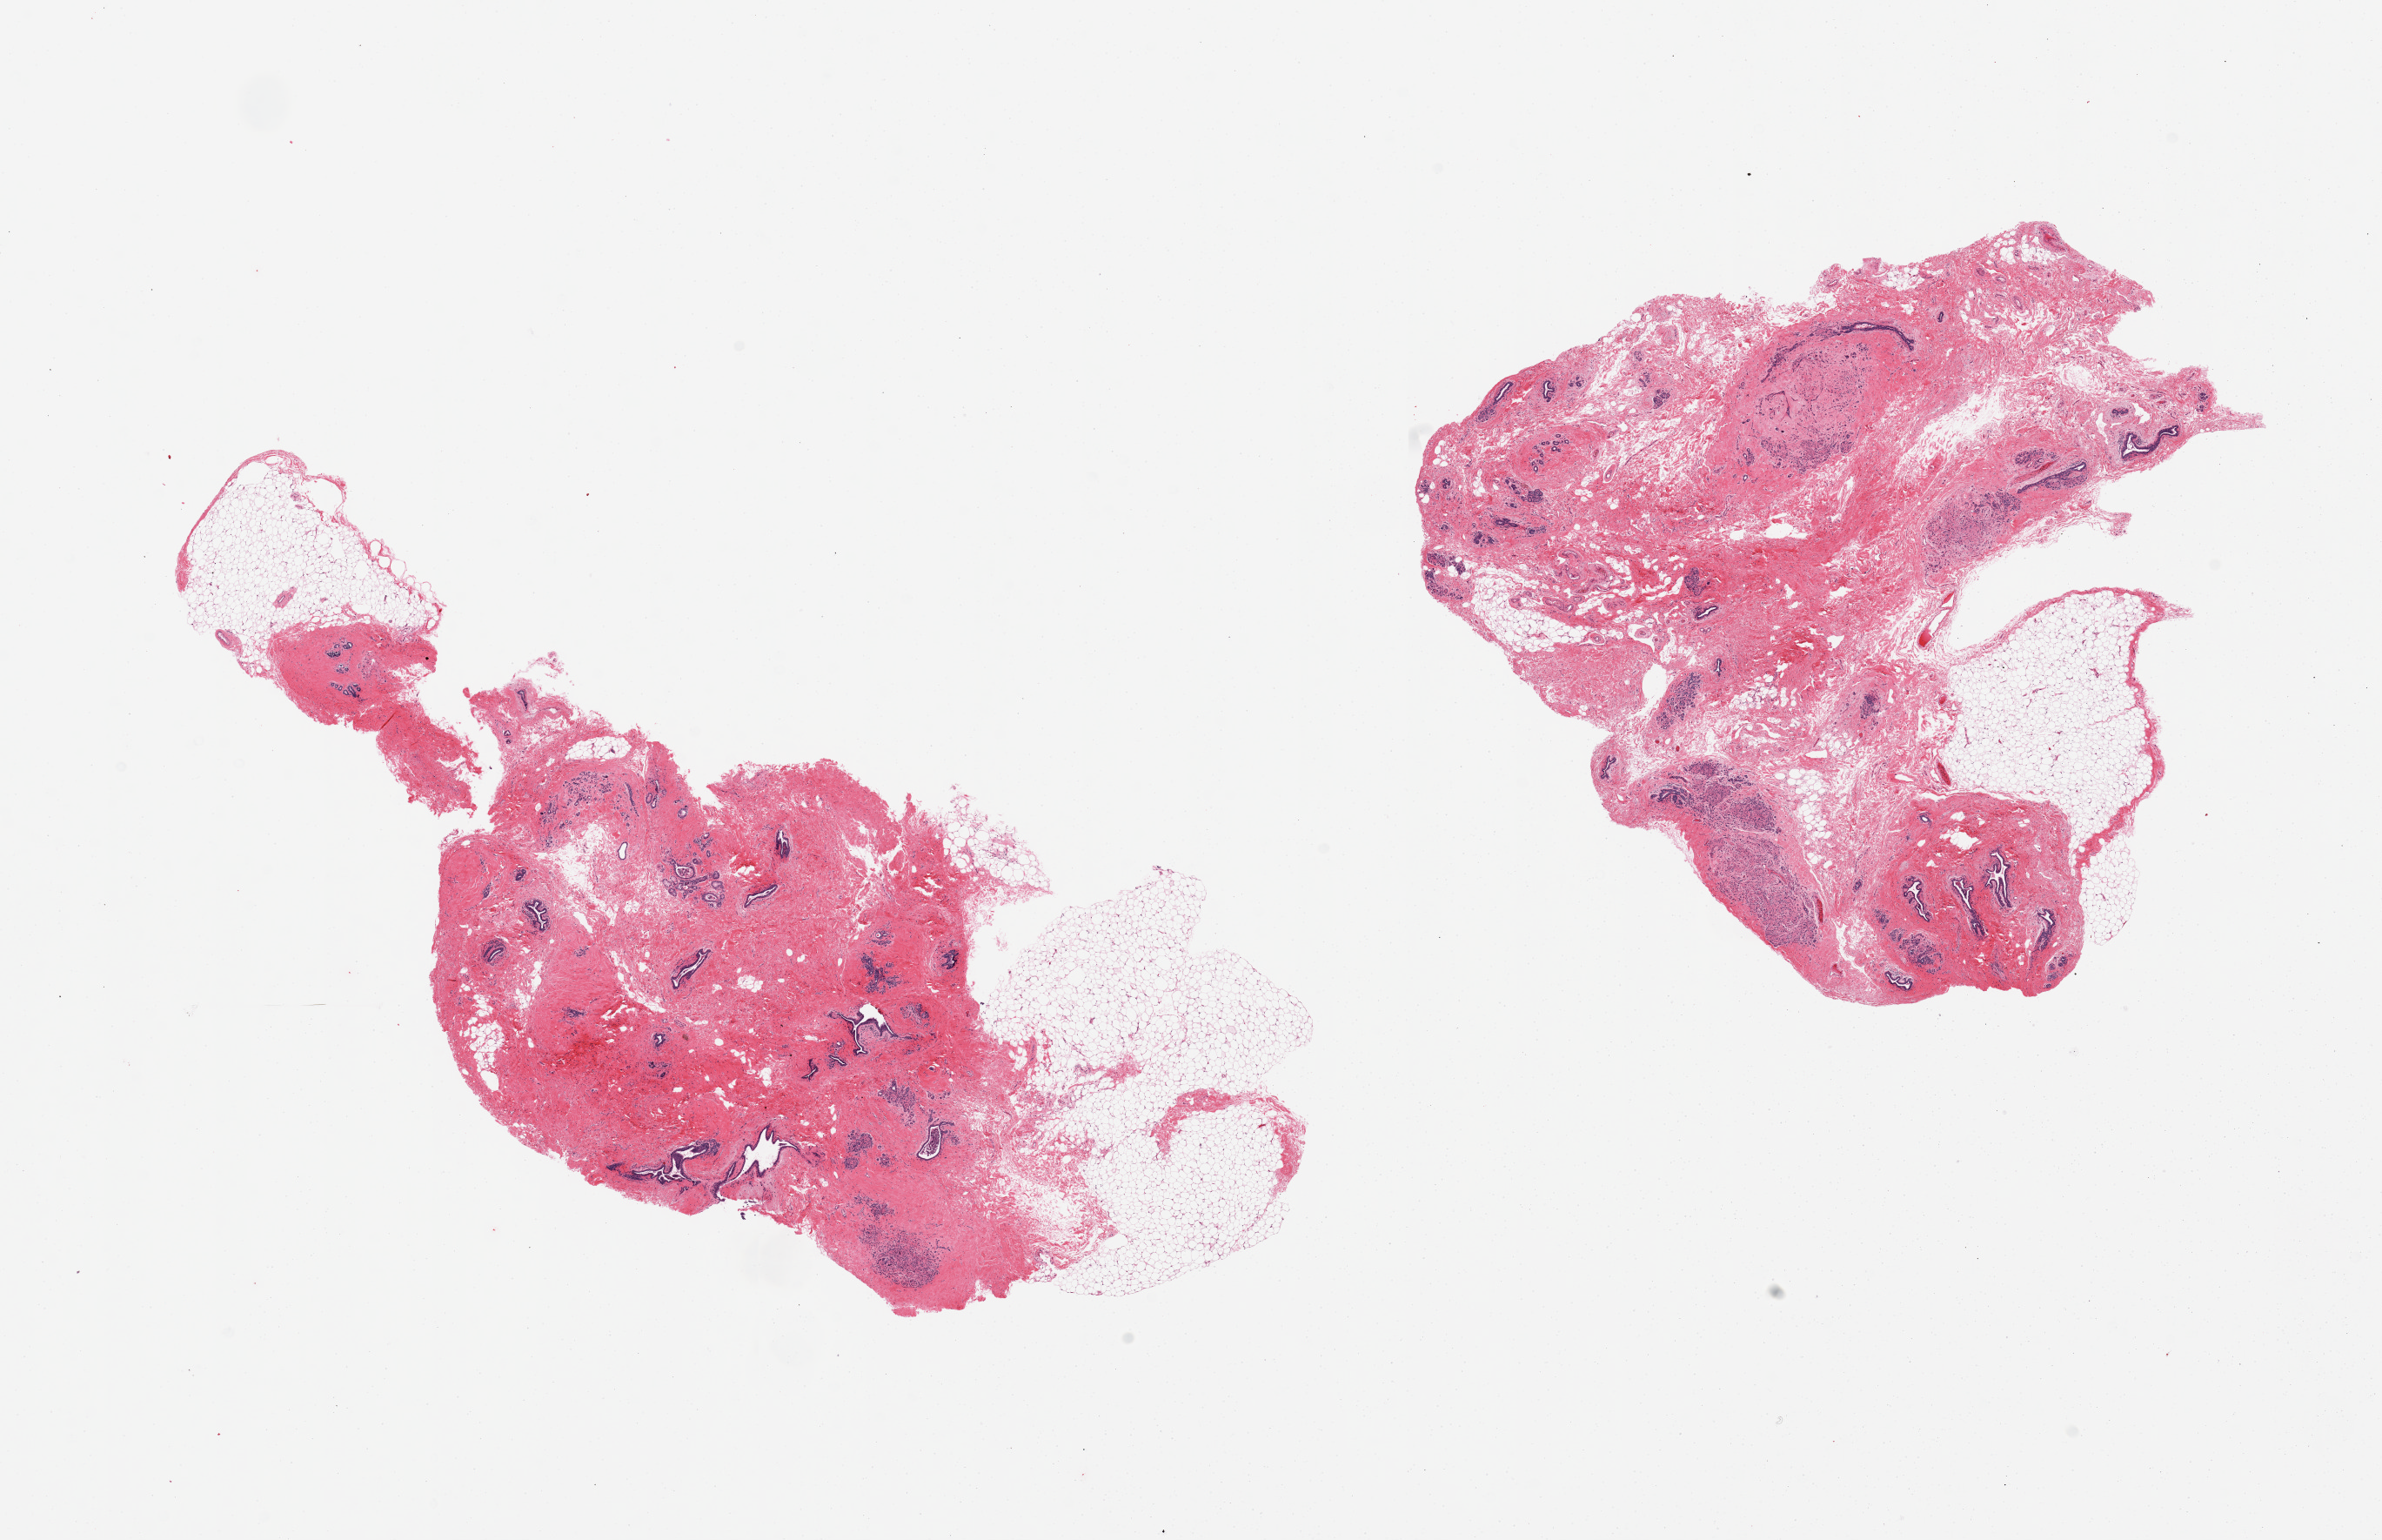
Digitized H&E-stained section — shown as a low-resolution overview of the whole scanned area (about 21.7 x 14.0 mm). PAXgene-fixed paraffin-embedded (PFPE) section. Target tissue: breast. Donor tissue sample. Female donor.
* reviewer comment on this tissue sample: 2 pieces; ductal and lobular units; some sclerosed lobules